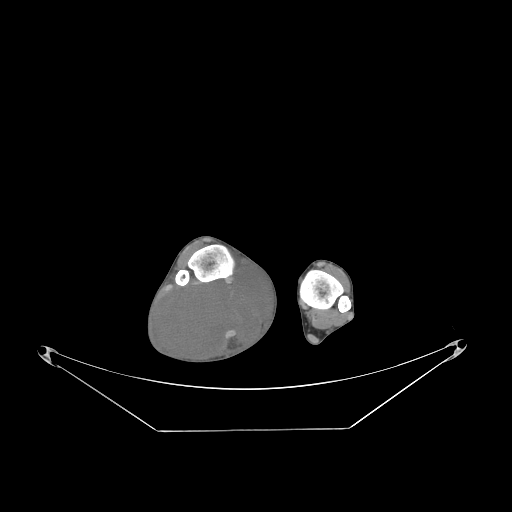
CT of an extremity soft-tissue mass (from a PET/CT study), one axial slice; slice 54 of 267 in the series (ordered by position); reconstruction kernel STANDARD; soft-tissue window (W 400 / L 40 HU); 3.75 mm slice thickness; 512 × 512 image matrix, field of view 500 × 500 mm. Male patient. Case-level facts recorded for this patient, not image findings: histological type: liposarcoma - round cell; grade: high; site of the primary tumour: right calf.
Outlined on this slice (expert contour drawn on MRI and transferred to this co-registered scan by the dataset authors):
- gross tumour volume (mass): bounding box [x1, y1, x2, y2] px = [158, 270, 275, 364]